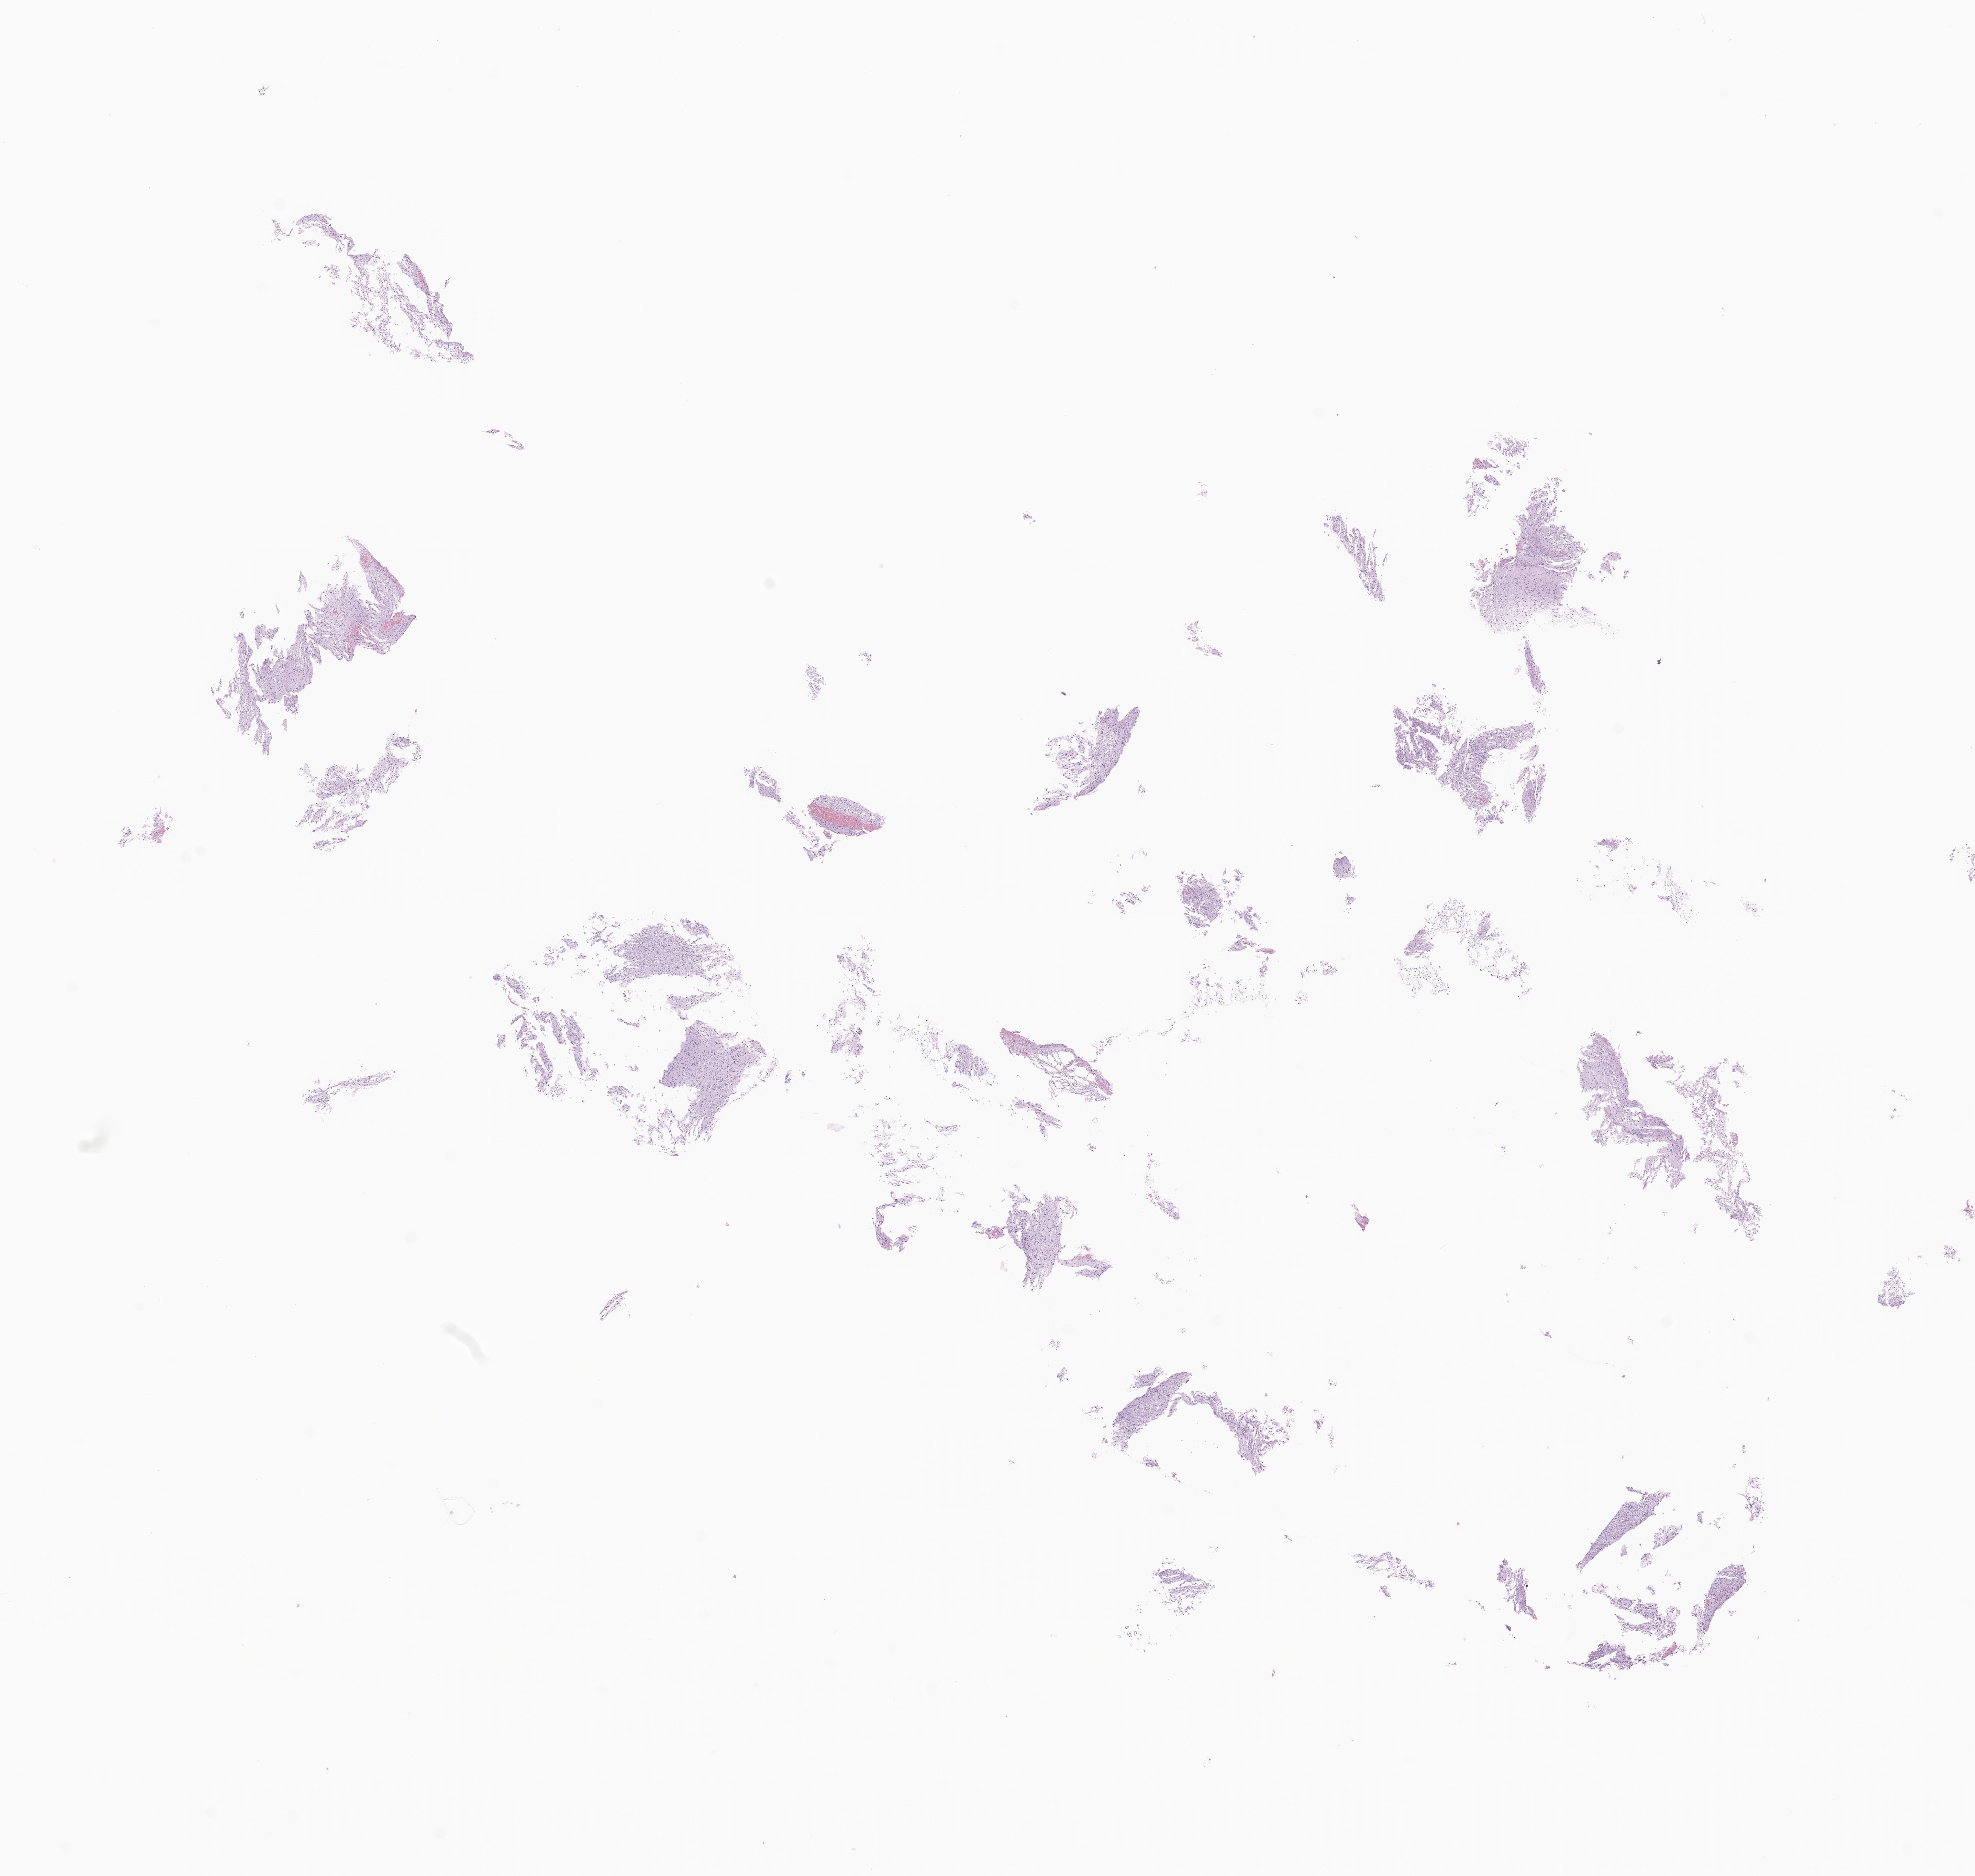
Digitized haematoxylin and eosin-stained section of tumor tissue from the frontal lobe, a low-resolution overview of the entire scanned area, about 17.4 x 16.5 mm. FFPE section. Male patient, age 195 months (16 years 3 months).
Recorded diagnosis: Glioma, malignant.